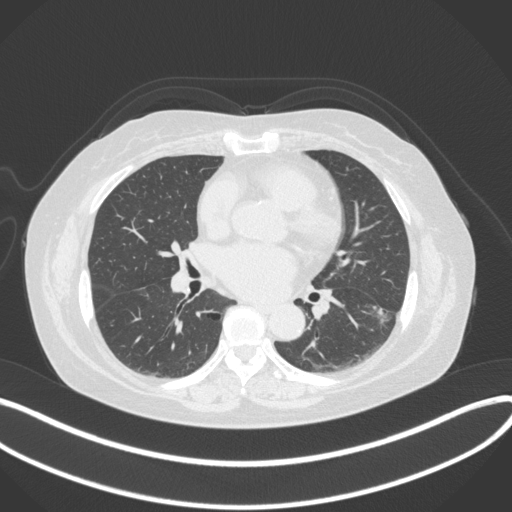
Chest CT, one axial slice. Slice 177 of 373 in the series (ordered by position). Reconstruction kernel B31f. 120 kVp. Lung window (W 1500 / L -600 HU). 1 mm slice thickness. 512 × 512 image matrix. Patient: female, 67 years. Case-level facts recorded for this patient, not image findings: clinical TNM (as recorded): T1c N0 M0.
Structures marked on this image (bounding box drawn by a radiologist):
- lung tumour (recorded histology: adenocarcinoma): bounding box <365,300,397,332> (left, top, right, bottom; pixels)